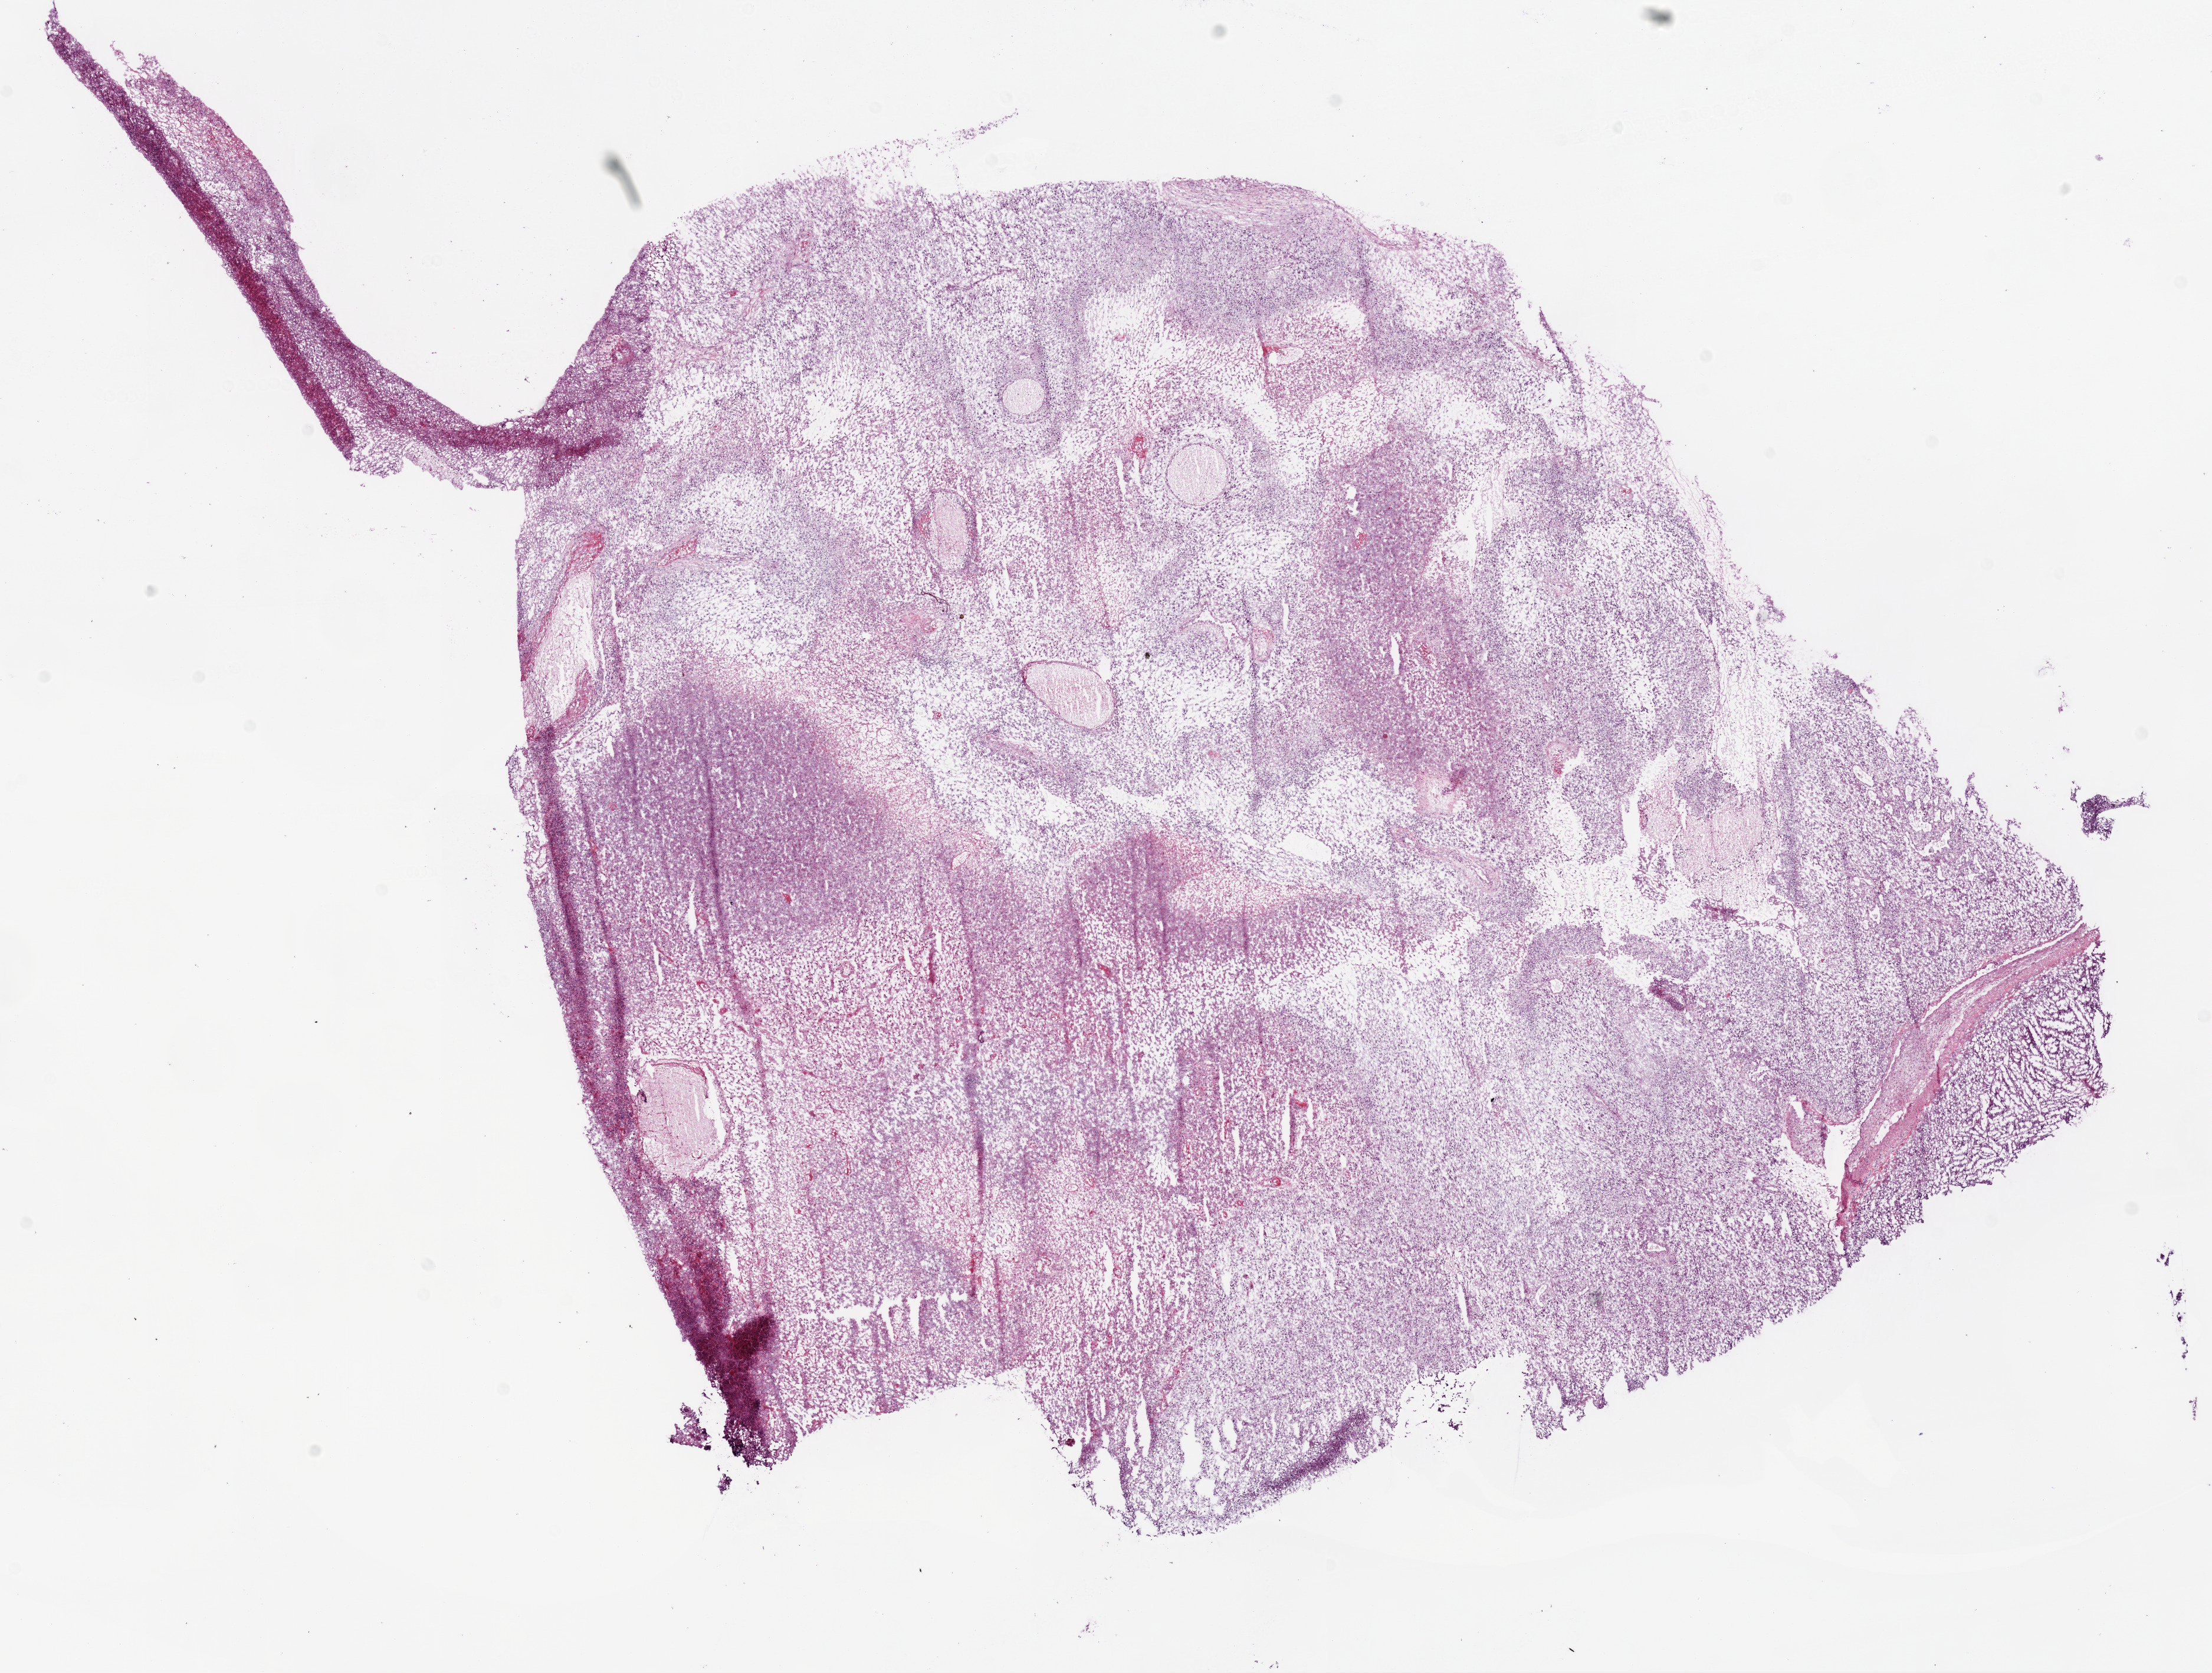
H&E whole-slide image — a low-resolution overview of the entire scanned area, about 15.0 x 11.4 mm; frozen section from the bottom of the tissue portion; sample: primary tumour, brain. Patient: female, age at initial diagnosis 61 years. Pathologist review of this section (percent, as recorded): tumour cells 60%, tumour nuclei 90%, normal cells 0%, stromal cells 10%, necrosis 30%.
- histologic diagnosis: Glioblastoma